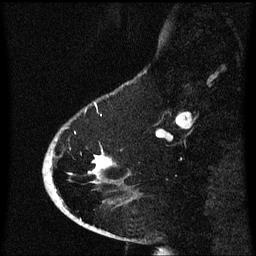
Breast MRI (dynamic contrast-enhanced), one sagittal slice; slice 15 of 60 in the series (ordered by position); dynamic contrast-enhanced series, image 2 of 3 at this slice position (ordered by acquisition); 1.5 T; TE 4.2 ms, TR 8.4 ms; 2.1 mm slice thickness; 256 × 256 image matrix, field of view 200 × 200 mm. Patient: female, 53 years. Case-level facts recorded for this patient, not image findings: setting: breast cancer imaged before/during neoadjuvant chemotherapy; receptor status: HR-positive, HER2-negative.
Structures marked on this image (semi-automatic segmentation, software-assisted and operator-edited):
- analysis volume of interest (the breast-tissue region the enhancement analysis was run in; not a lesion): bounding box (x1, y1, x2, y2) in pixels: (49, 128, 132, 201)
- tumour enhancement mask (voxels above the 70 % enhancement threshold inside the analysis volume of interest): (92, 154, 113, 173)